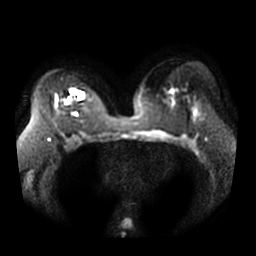
Breast MRI, one axial slice; diffusion-weighted series; image 2 of 4 stored at this slice position (different b-values; order by instance number); 3 T; 5 mm slice thickness; 256 × 256 image matrix. Female patient.
Outlined on this slice (manually delineated by an expert):
- tumour on diffusion-weighted imaging: bounding box <75,91,82,98> (left, top, right, bottom; pixels)